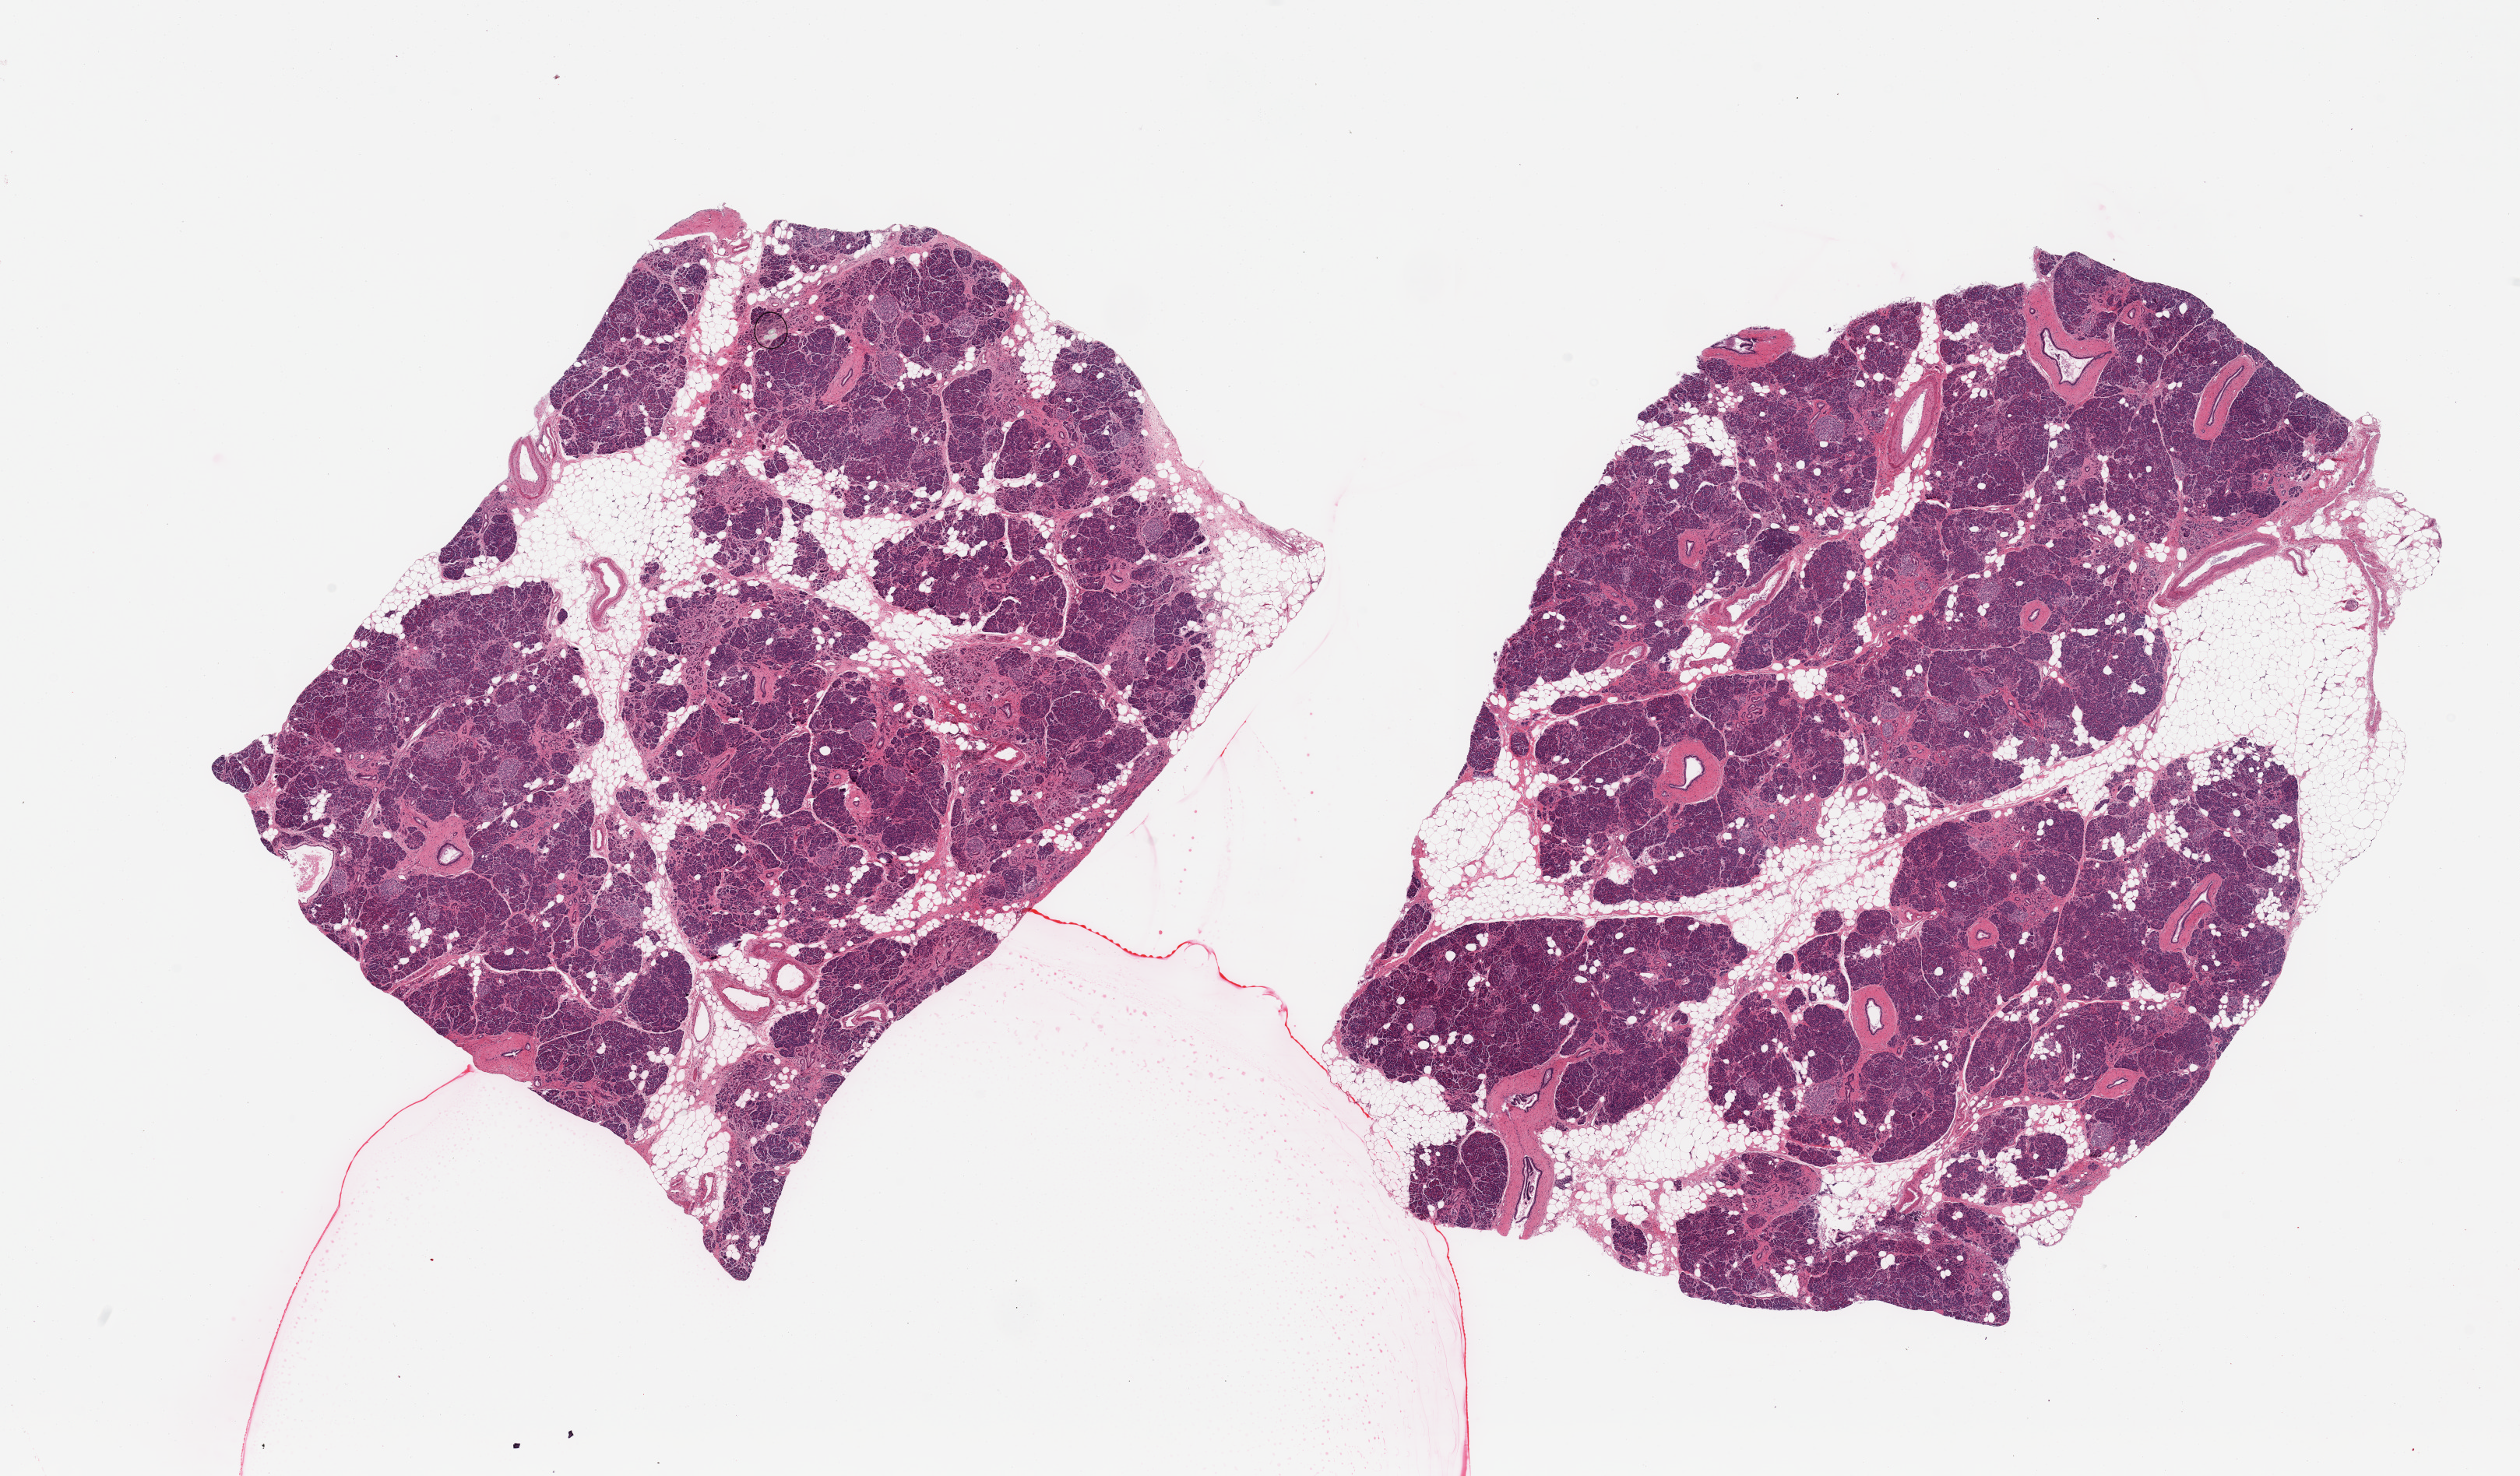
Whole-slide image, hematoxylin and eosin (H&E) stain, low-resolution overview of the scanned area, about 25.6 x 15.0 mm (from a 20x scan), PAXgene-fixed, paraffin-embedded tissue, section of pancreas (target tissue), tissue donor sample. Donor: male.
Reviewer comment on this tissue sample: 2 pieces, islets well-preserved; Fibrosis and ductal proliferations consistent with remote pancreatitis.